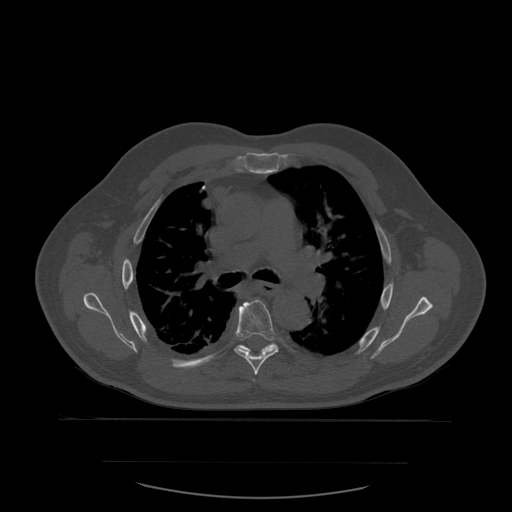
CT including the spine, one axial slice. Slice 401 of 590 in the series (ordered by position). Bone window (W 1800 / L 400 HU). 512 × 512 image matrix, field of view 479 × 479 mm. Patient age 71 years. From the clinical record (not read from this slice): primary cancer: lung.
Structures marked on this image (semi-automatically segmented with operator editing):
- T6 vertebra: box from (x=234, y=300) to (x=279, y=375) px
- T7 vertebra: (x=238, y=343)–(x=276, y=353)